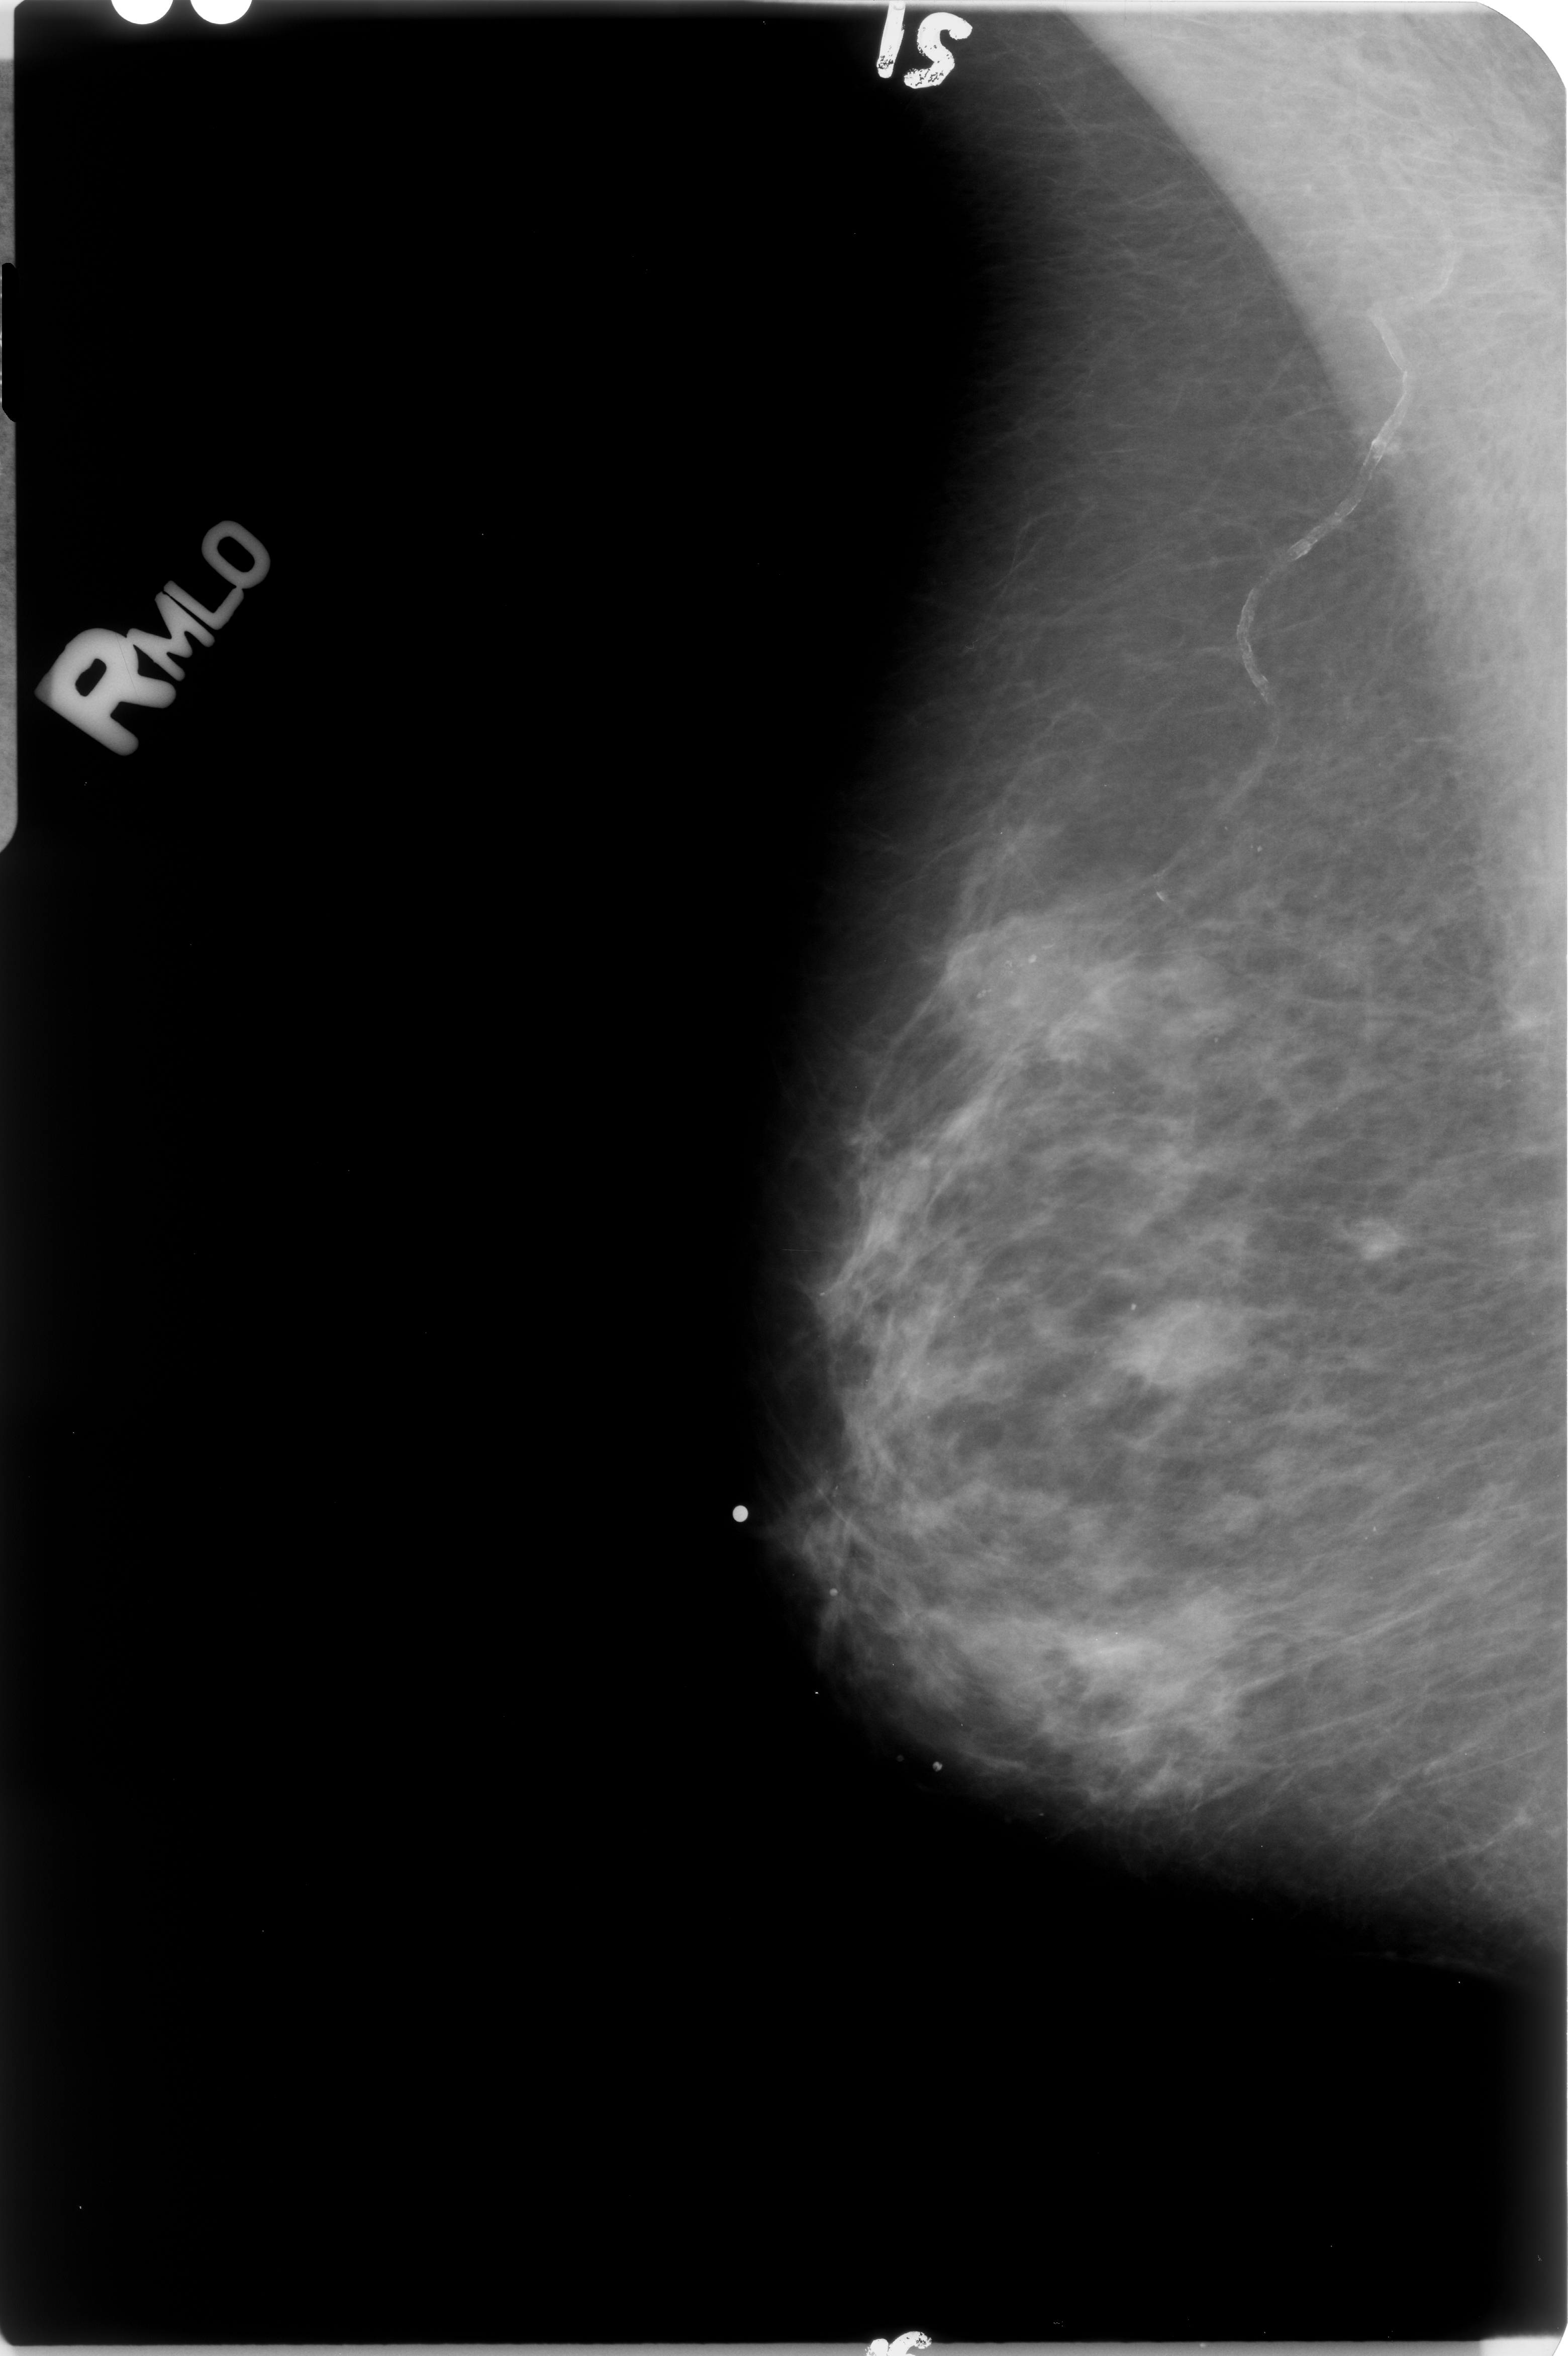
Scanned film-screen mammogram. Right breast. Mediolateral oblique (MLO) view. 1568 × 2356 image matrix.
Expert-marked regions of interest on this image (one box per marked abnormality):
- calcifications, morphology pleomorphic, distribution clustered; BI-RADS assessment category 4; subtlety rating 3 on a 1 (subtle) to 5 (obvious) scale; pathology (as recorded): malignant: bounding box <936,904,1243,1070> (left, top, right, bottom; pixels)